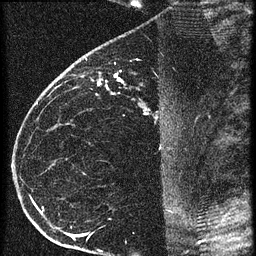
Breast MRI (dynamic contrast-enhanced), one sagittal slice. Position 38 of 60 along the scan axis. 3 images stored at this slice position (order not interpretable as contrast timing). 1.5 T. TE 4.2 ms, TR 20.4 ms. 1.5 mm slice thickness. 256 × 256 image matrix, field of view 180 × 180 mm. Female patient, age 35 years. Case-level facts recorded for this patient, not image findings: setting: breast cancer imaged before/during neoadjuvant chemotherapy; receptor status: HR-positive, HER2-negative.
Annotated regions visible in this slice (semi-automatic segmentation, software-assisted and operator-edited):
- analysis volume of interest (the breast-tissue region the enhancement analysis was run in; not a lesion): bounding box [x1, y1, x2, y2] px = [65, 60, 169, 119]
- tumour enhancement mask (voxels above the 90 % enhancement threshold inside the analysis volume of interest): [98, 74, 148, 115]